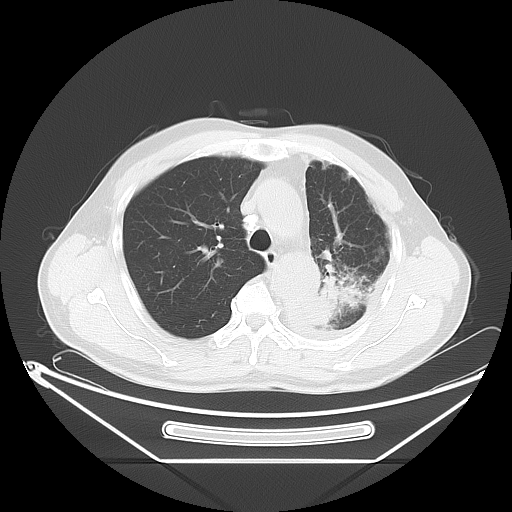
Chest CT, one axial slice. Position 44 of 63 along the scan axis. Lung window (W 1500 / L -600 HU). 5 mm slice thickness. 512 × 512 image matrix, field of view 442 × 442 mm. Male patient, age 60 years. From the clinical record (not read from this slice): clinical TNM (as recorded): T4 N1 M1.
Annotated regions visible in this slice (bounding box drawn by a radiologist):
- lung tumour (recorded histology: adenocarcinoma): bounding box <295,268,369,336> (left, top, right, bottom; pixels)